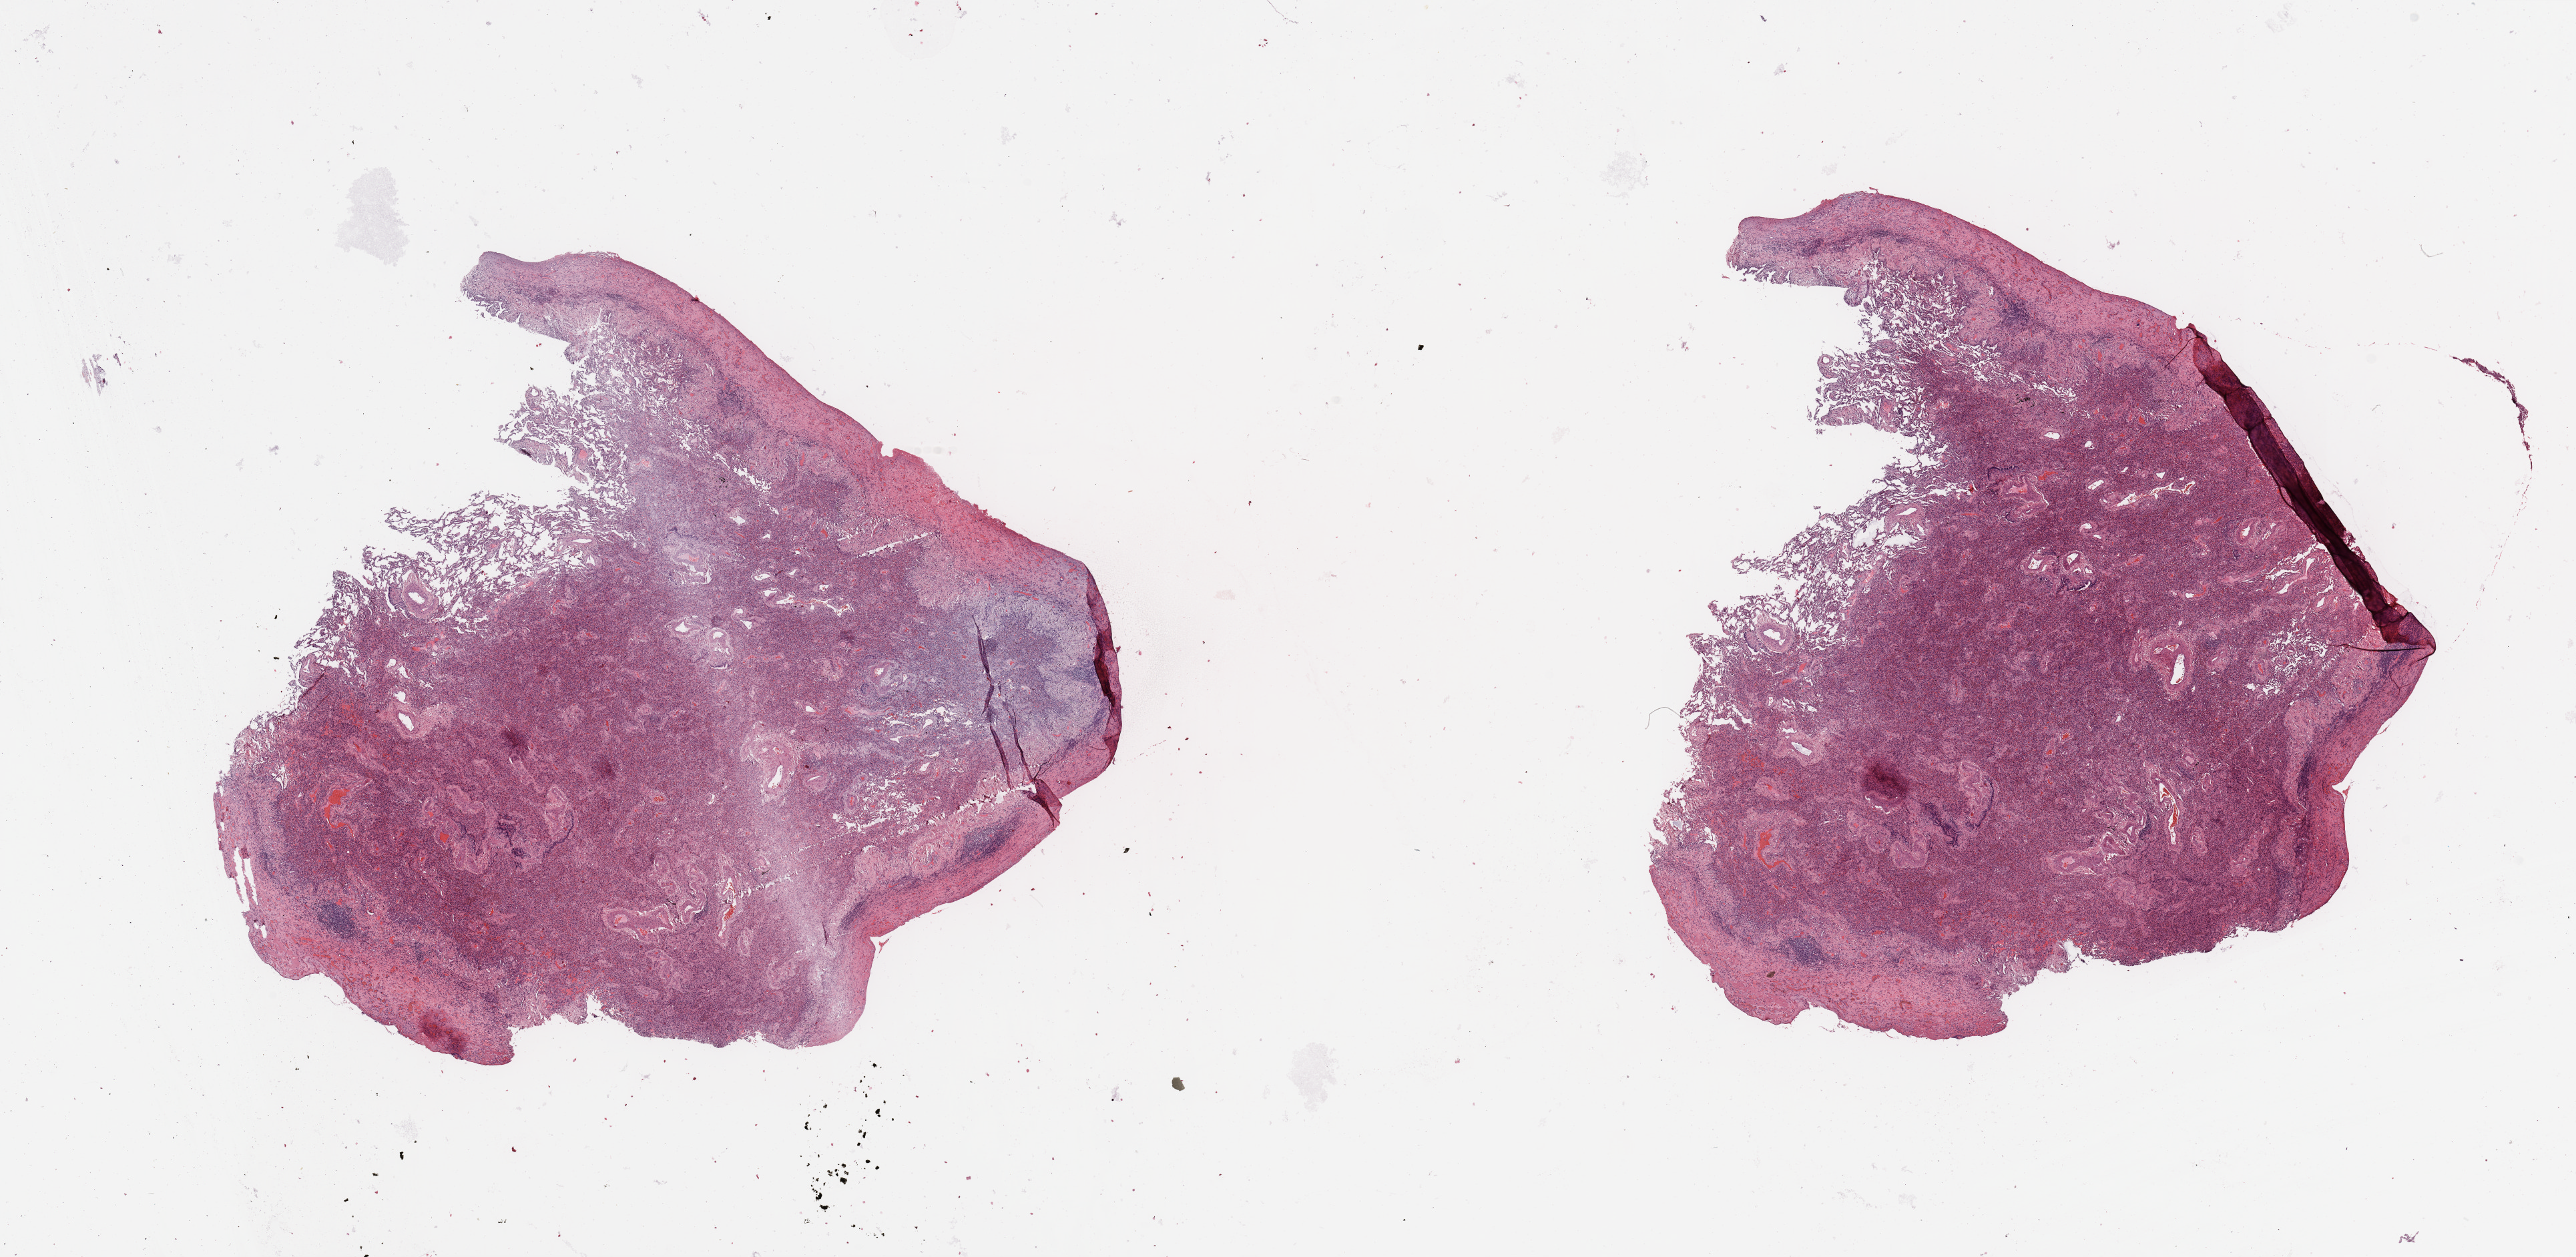
Hematoxylin and eosin (H&E) stained whole-slide image — whole scanned area (about 30.5 x 14.9 mm) shown as a low-resolution overview. Normal (non-tumour) tissue sample, lung. Patient: male, age 39 years.
- this section: normal (non-tumour) tissue from the same patient
- patient diagnosis: Adenocarcinoma, NOS